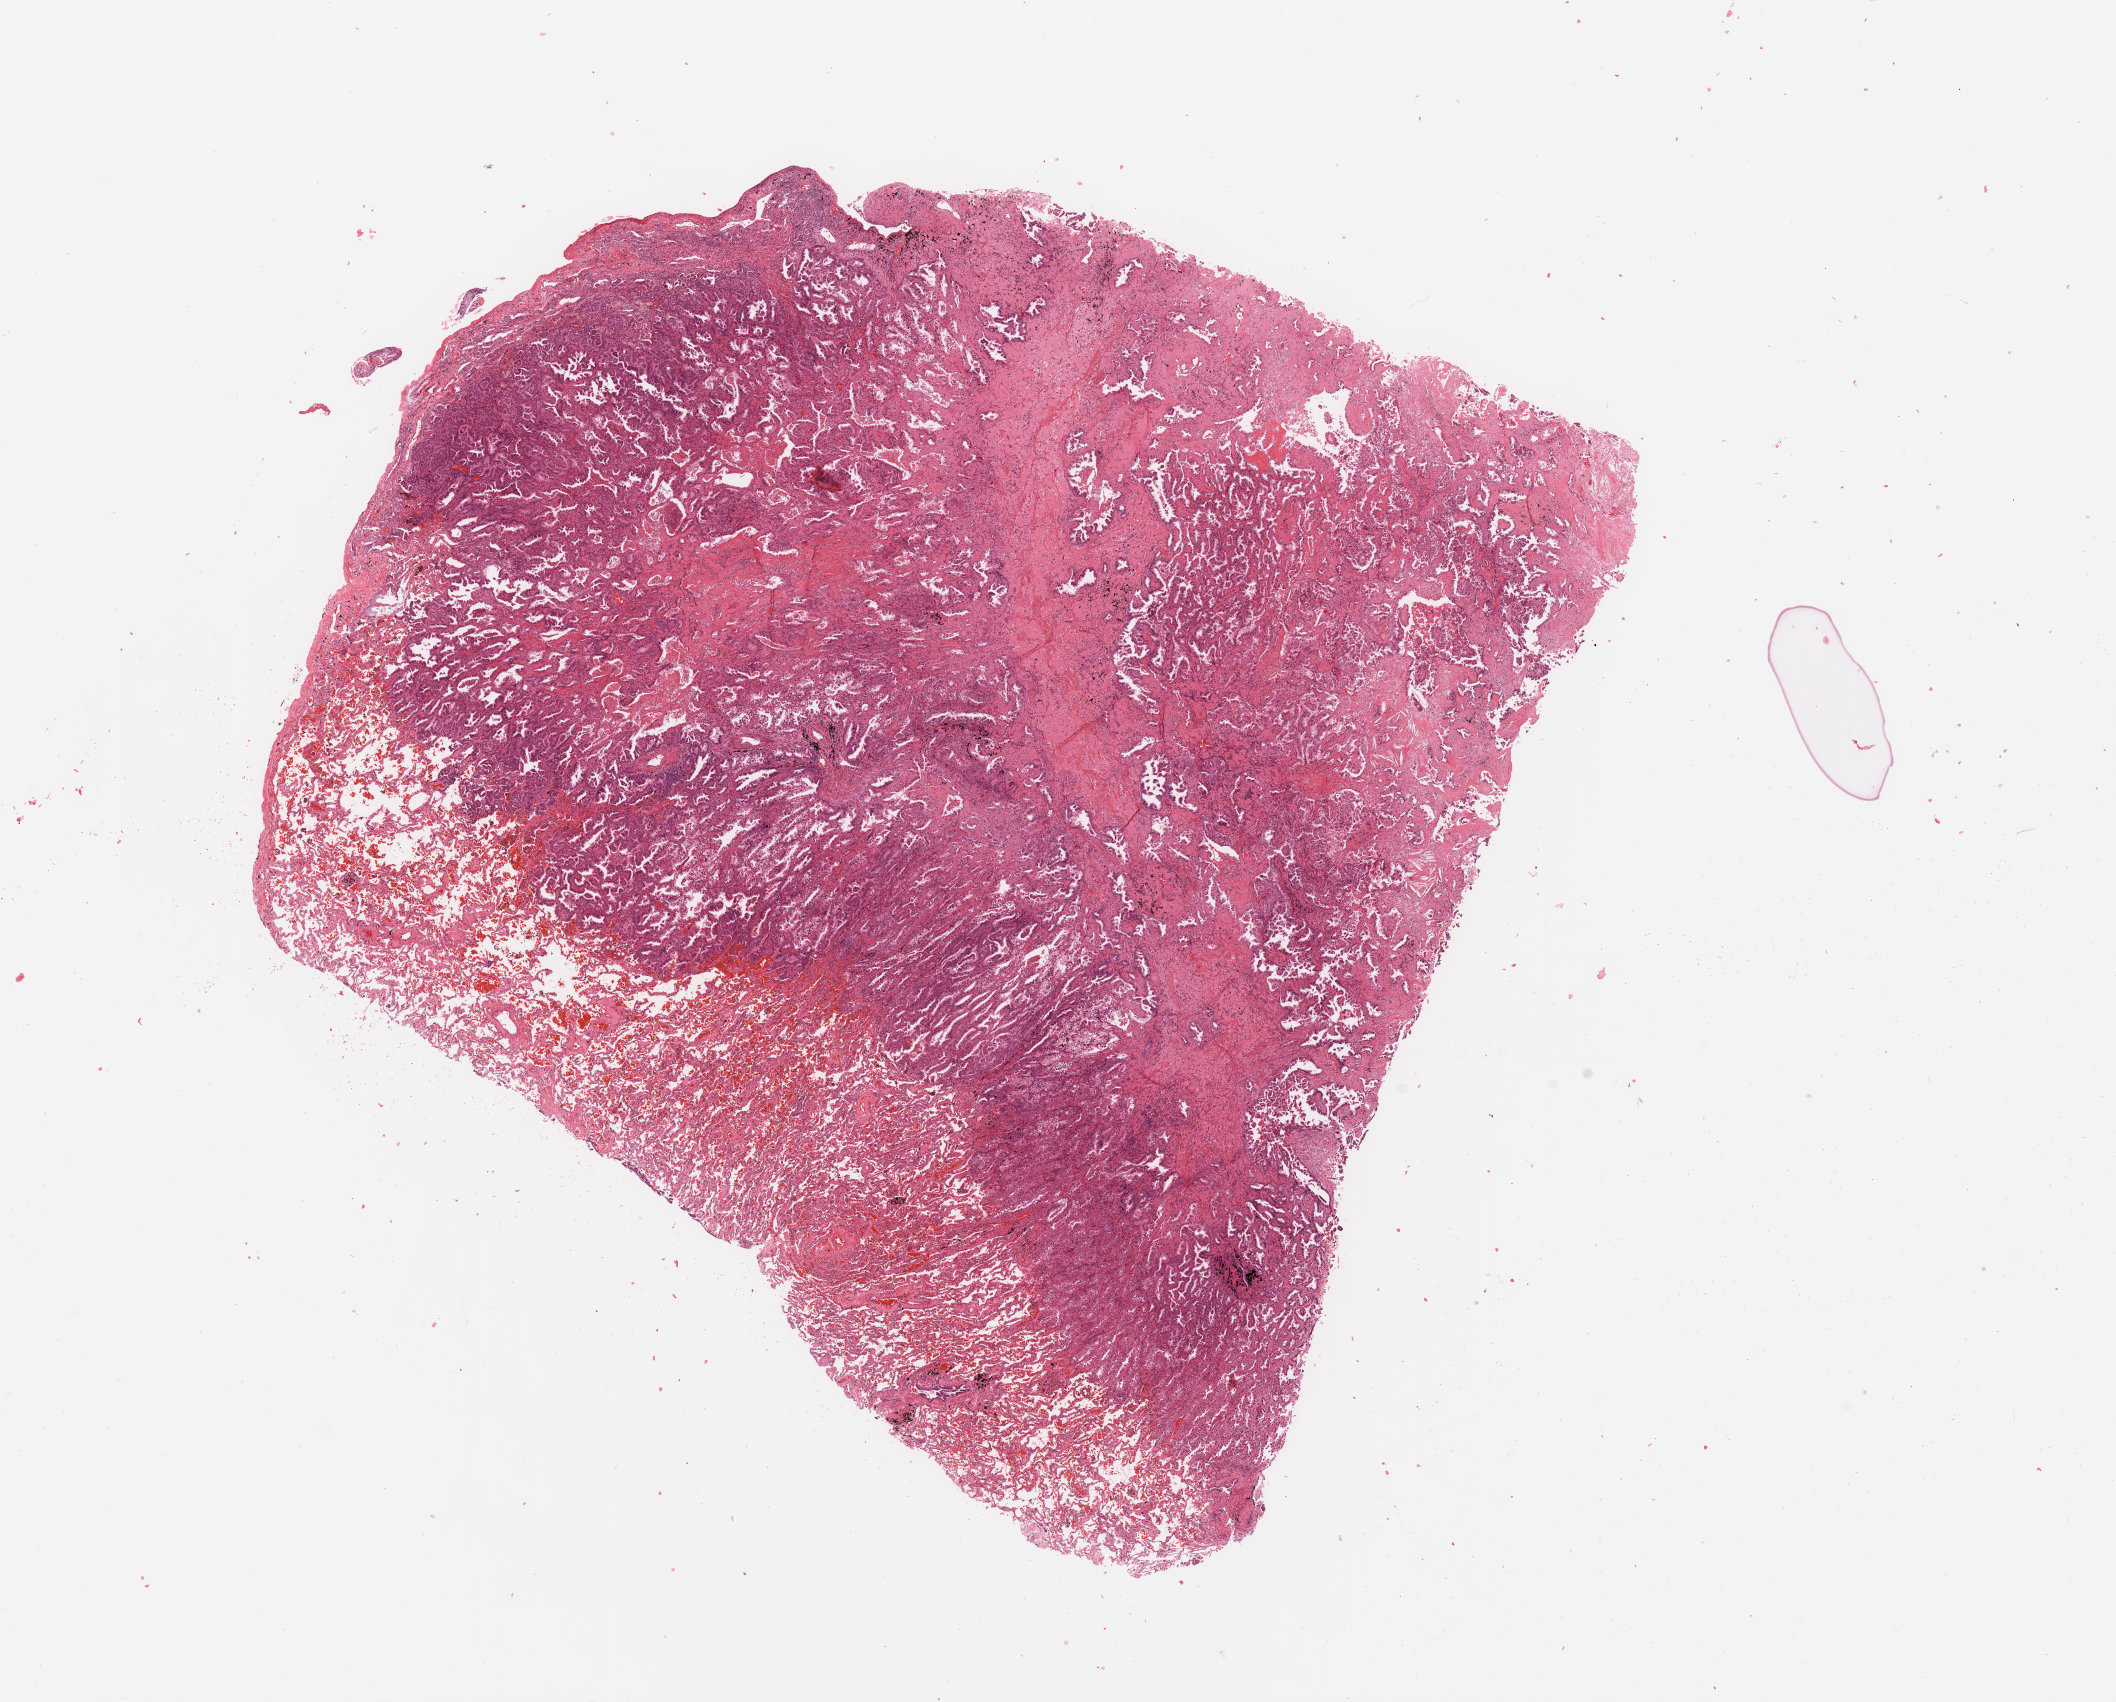
Whole-slide histology image, H&E-stained — low-resolution overview of the scanned area, about 16.7 x 13.5 mm (from a 20x scan), lung, tumour tissue. Female, 44 y/o. Histologic grade: G2 (moderately differentiated).
Diagnosis: Adenocarcinoma, NOS. AJCC pathologic stage: IIIA.